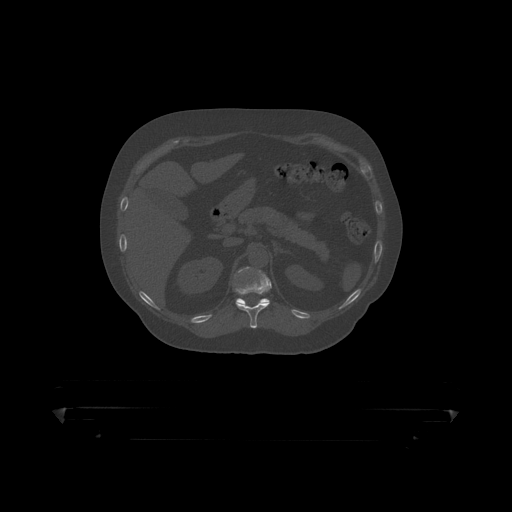
CT including the spine, one axial slice. Slice 186 of 390 in the series (ordered by position). Reconstruction kernel STANDARD. Bone window (W 1800 / L 400 HU). 512 × 512 image matrix. Male patient, age 60 years. Case-level facts recorded for this patient, not image findings: primary cancer: prostate.
Structures marked on this image (semi-automatically segmented with operator editing):
- T11 vertebra: bounding box [x1, y1, x2, y2] px = [234, 270, 272, 319]
- T12 vertebra: [236, 267, 270, 305]